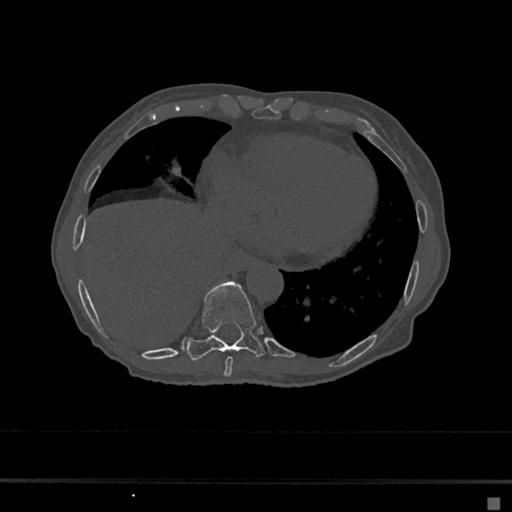
CT including the spine, one axial slice; position 279 of 797 along the scan axis; bone window (W 1800 / L 400 HU); 512 × 512 image matrix, field of view 360 × 360 mm. Patient: female, 68 years. From the clinical record (not read from this slice): primary cancer: renal.
Structures marked on this image (semi-automatically segmented with operator editing):
- T8 vertebra: bounding box [x1, y1, x2, y2] px = [224, 356, 233, 376]
- T9 vertebra: [188, 282, 264, 361]